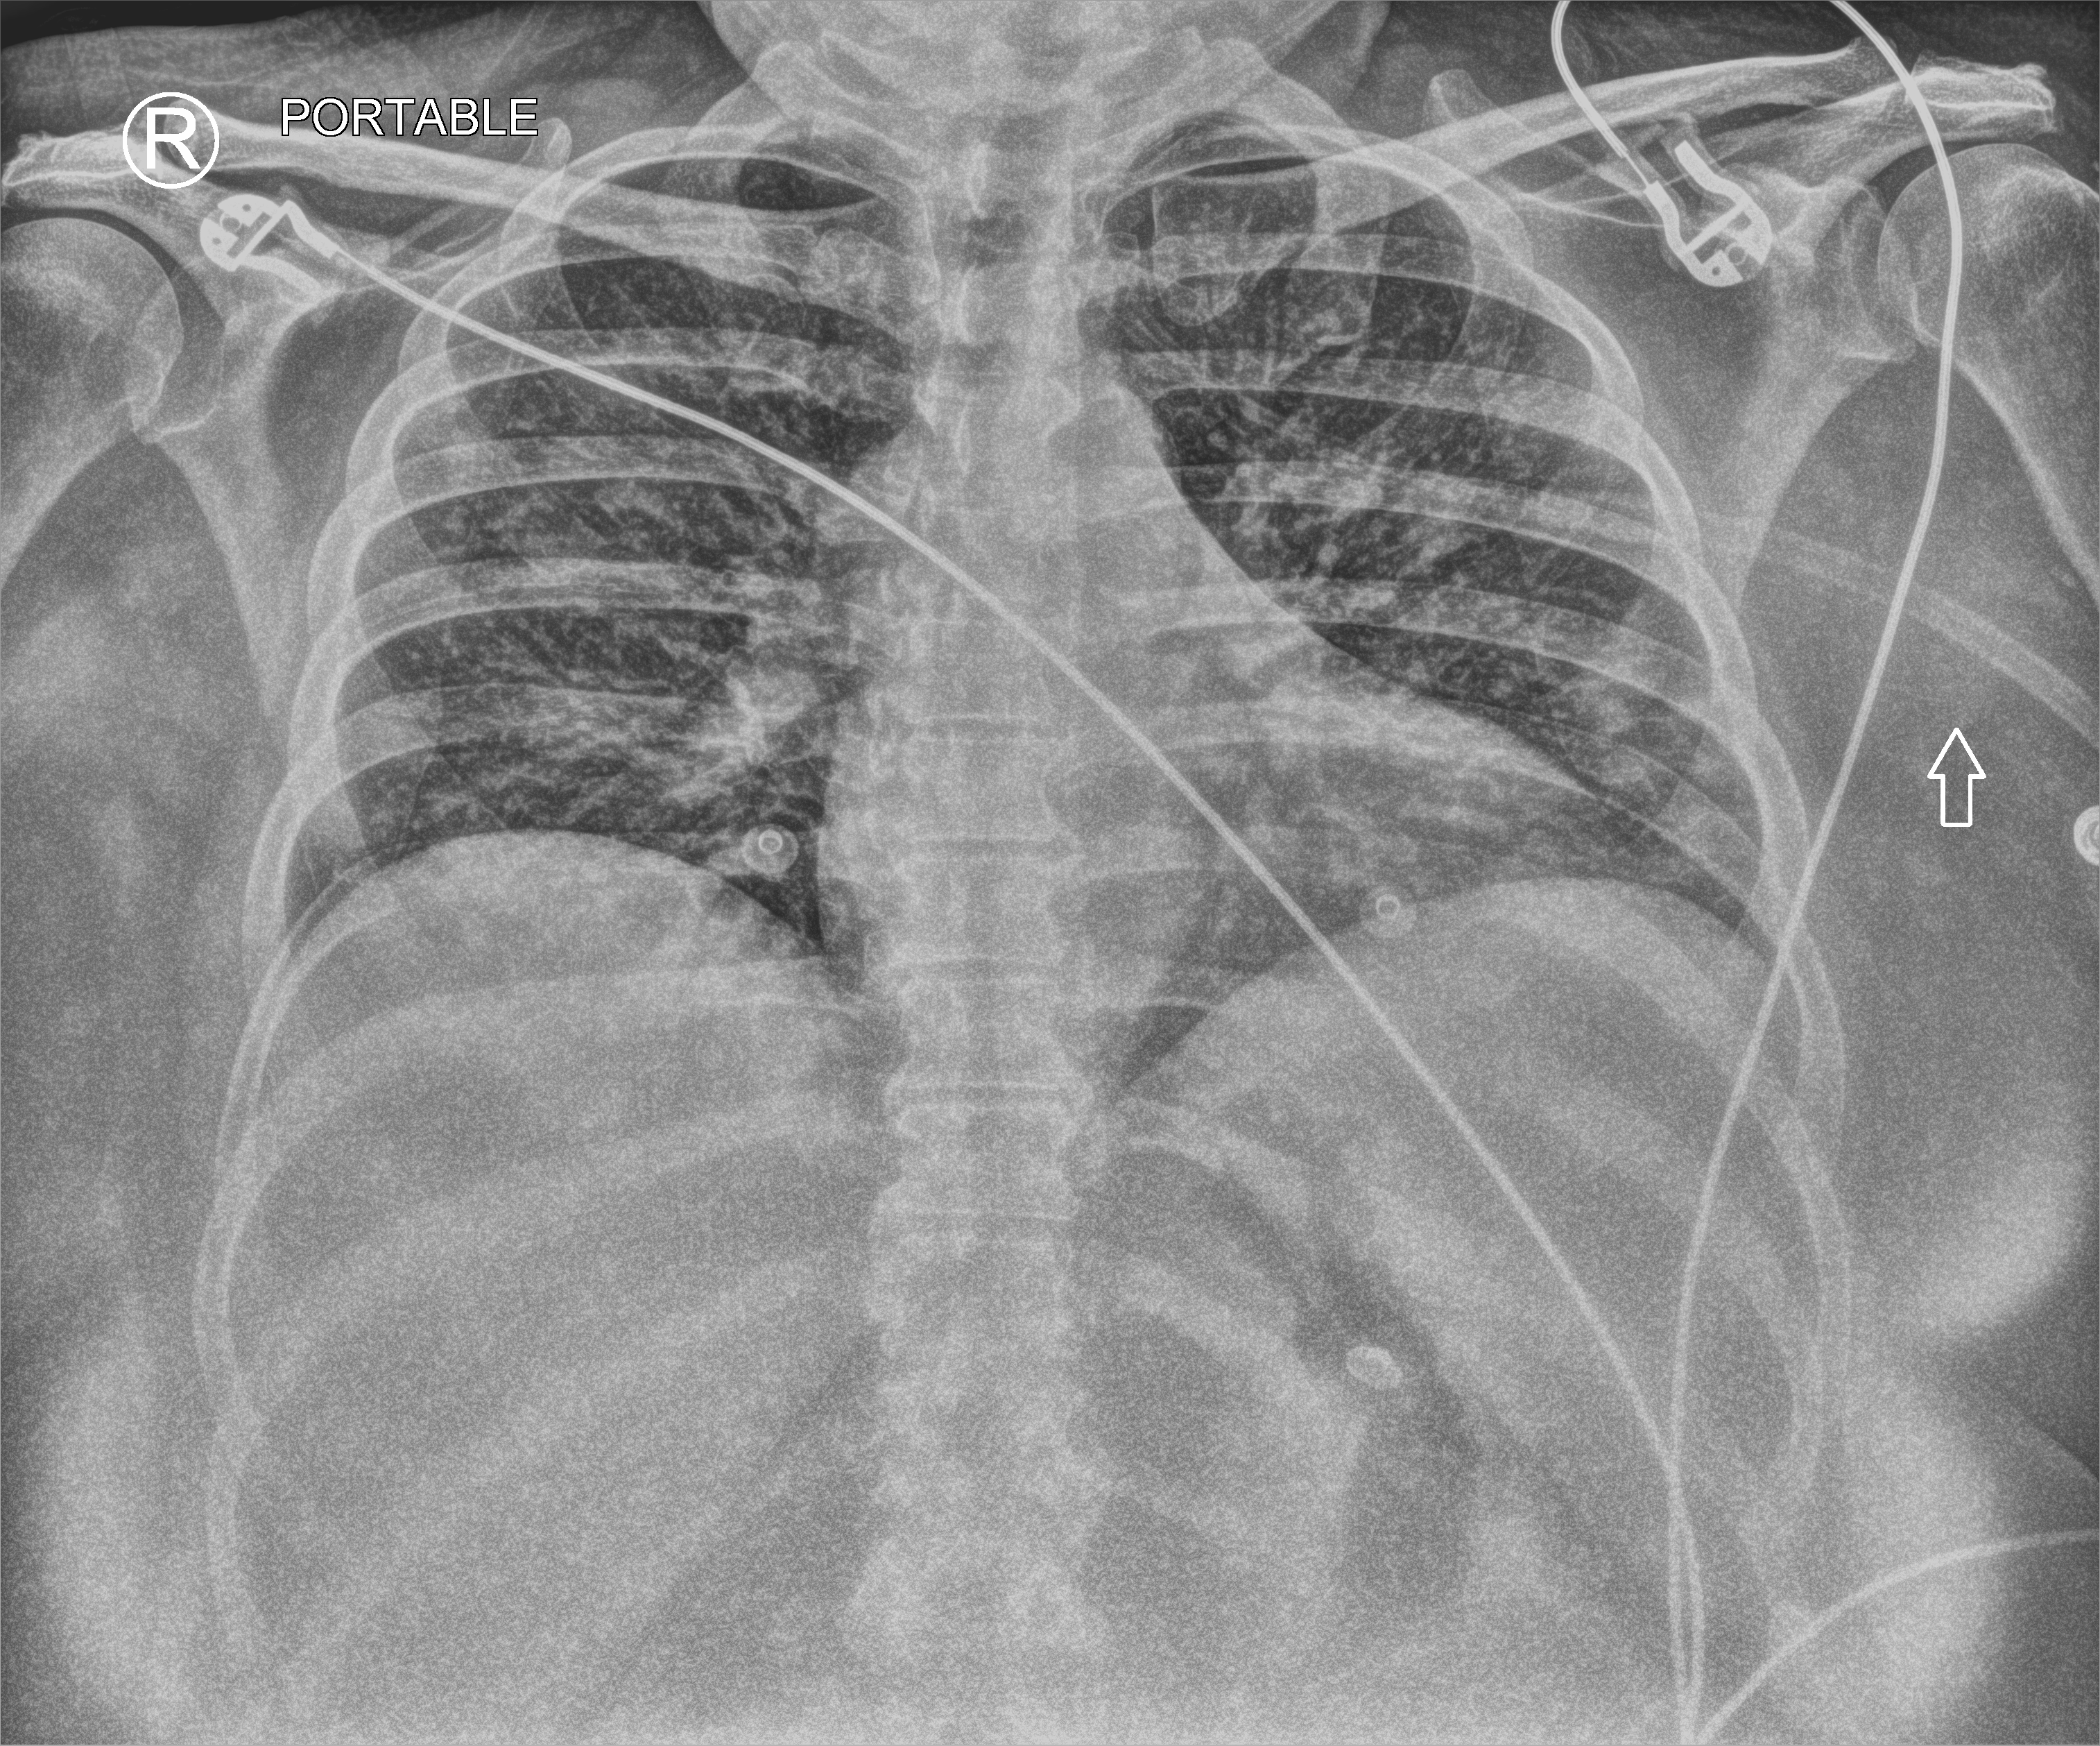
Chest X-ray (portable). Female patient hospitalised with COVID-19, age 18–59 years.
From the hospital-stay record, not from the radiograph (when in the stay this image was taken is not recorded): other chronic lung disease (admission record): yes.